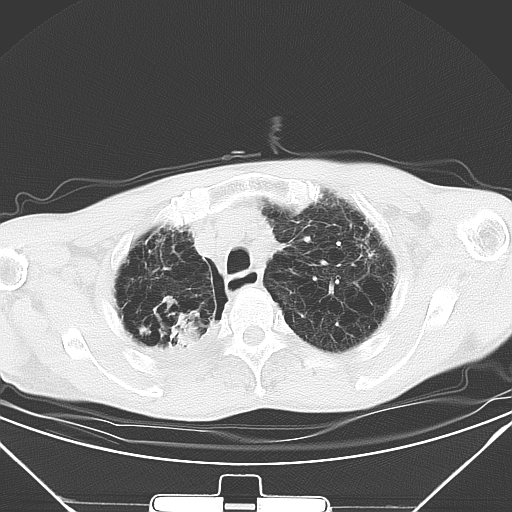
Chest CT, one axial slice. Slice 41 of 50 in the series (ordered by position). 120 kVp. Lung window (W 1500 / L -600 HU). 5 mm slice thickness. 512 × 512 image matrix, field of view 373 × 373 mm. Male patient, age 65 years. From the clinical record (not read from this slice): clinical TNM (as recorded): T3 N1 M1a.
Annotated regions visible in this slice (bounding box drawn by a radiologist):
- lung tumour (recorded histology: squamous cell carcinoma): bounding box <162,307,205,350> (left, top, right, bottom; pixels)